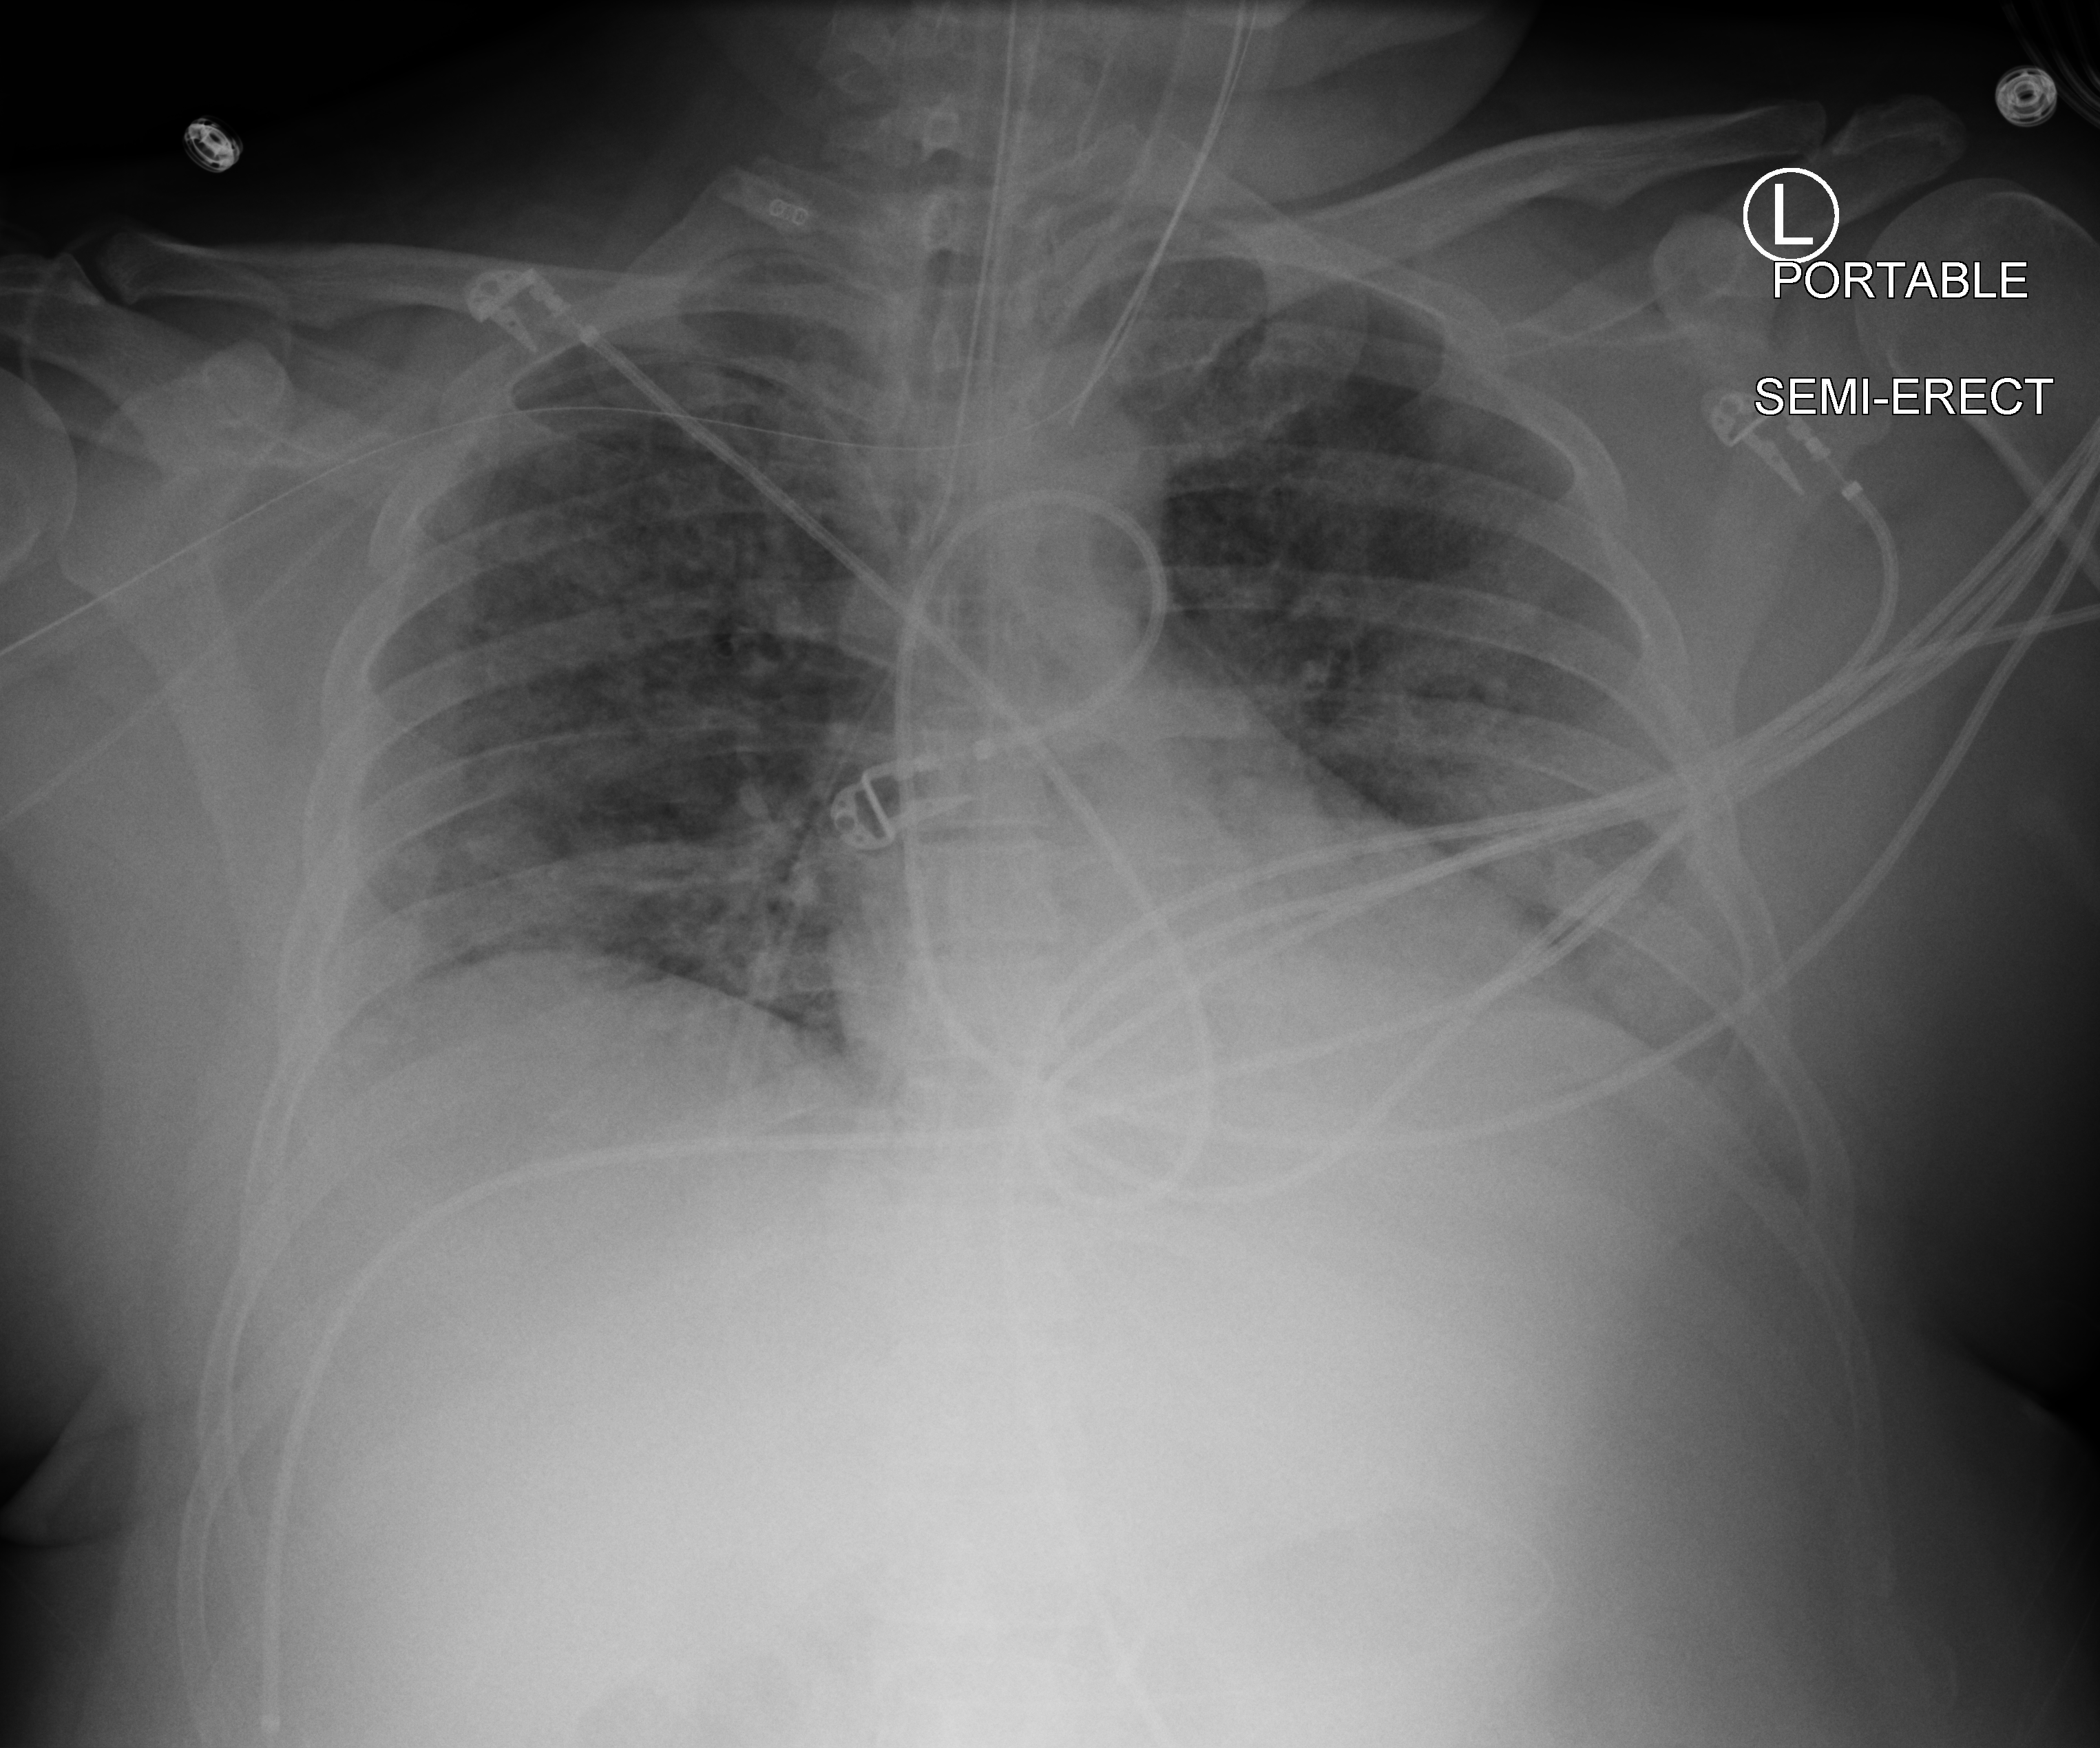
Bedside chest radiograph (computed radiography), anteroposterior (AP) projection. Patient hospitalised with COVID-19; male, aged 18–59 years.
From the hospital-stay record, not from the radiograph (when in the stay this image was taken is not recorded): admitted to intensive care during this hospital stay: yes; mechanically ventilated during this hospital stay: yes.